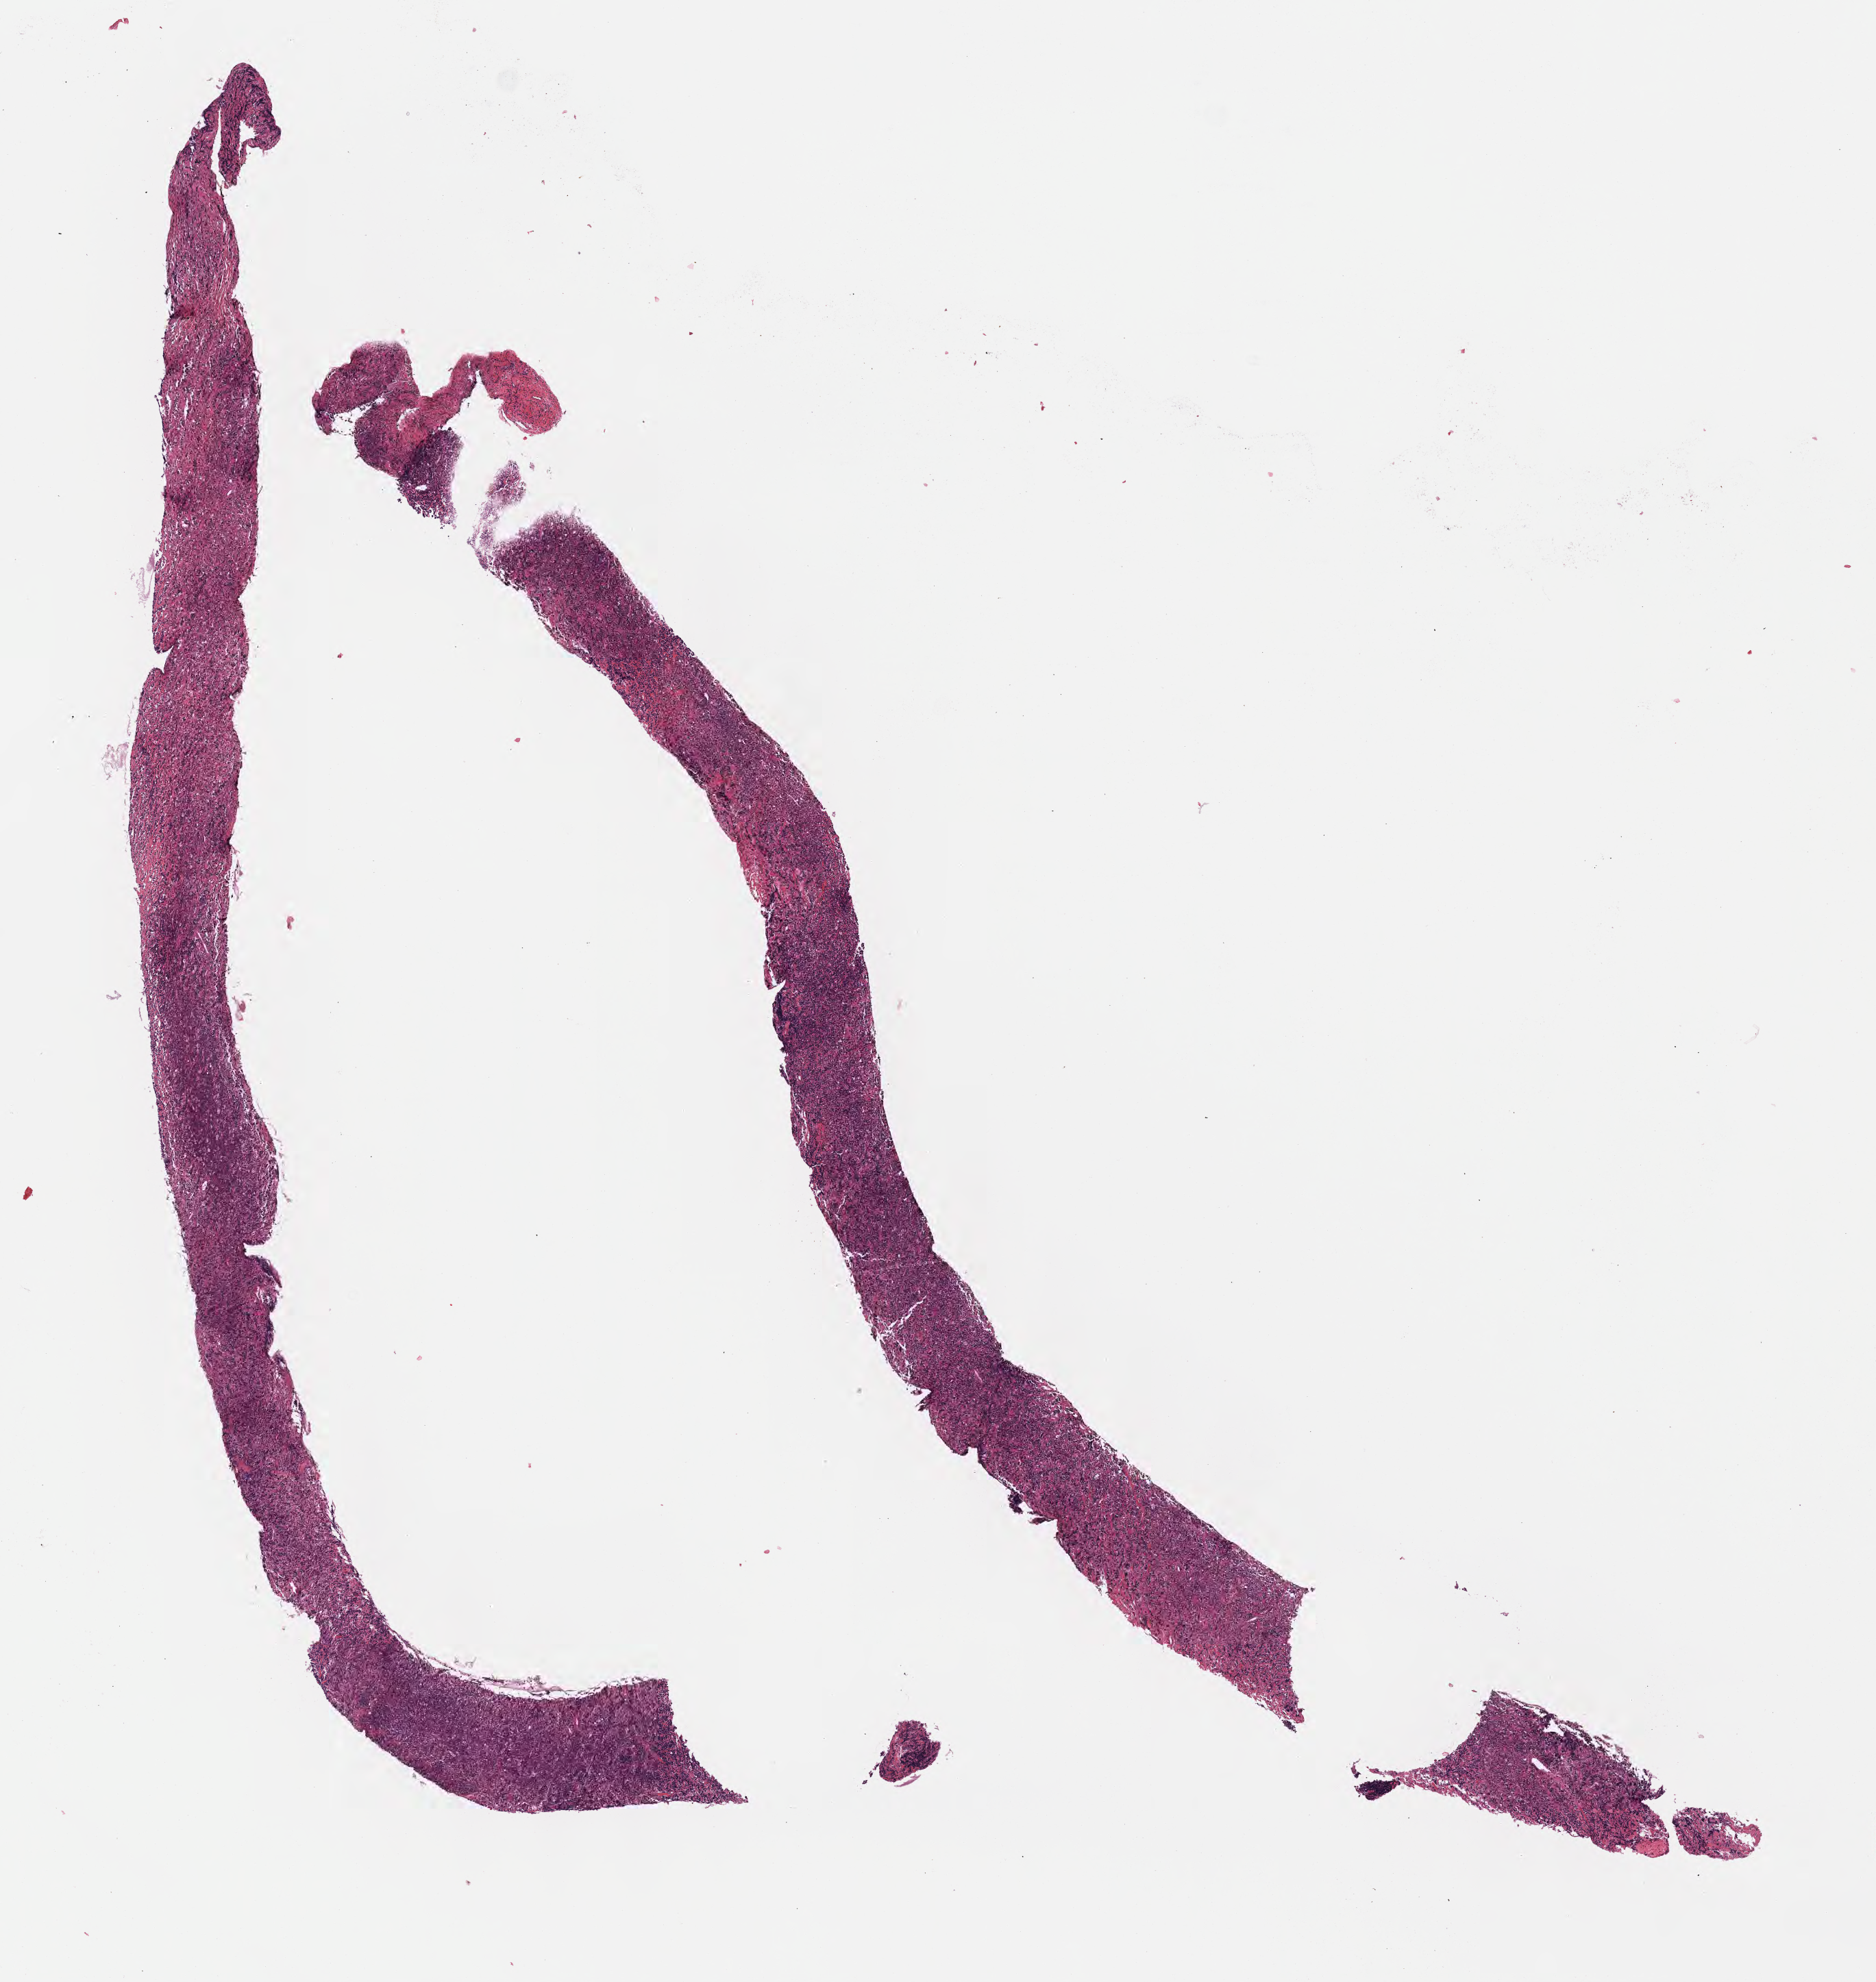
Haematoxylin and eosin whole-slide image — a low-resolution overview of the entire scanned area, about 11.1 x 11.7 mm. Specimen: tumor tissue. Site: abdomen proper. Male patient; age at initial diagnosis 9 years.
Histologic diagnosis: Burkitt lymphoma, NOS.